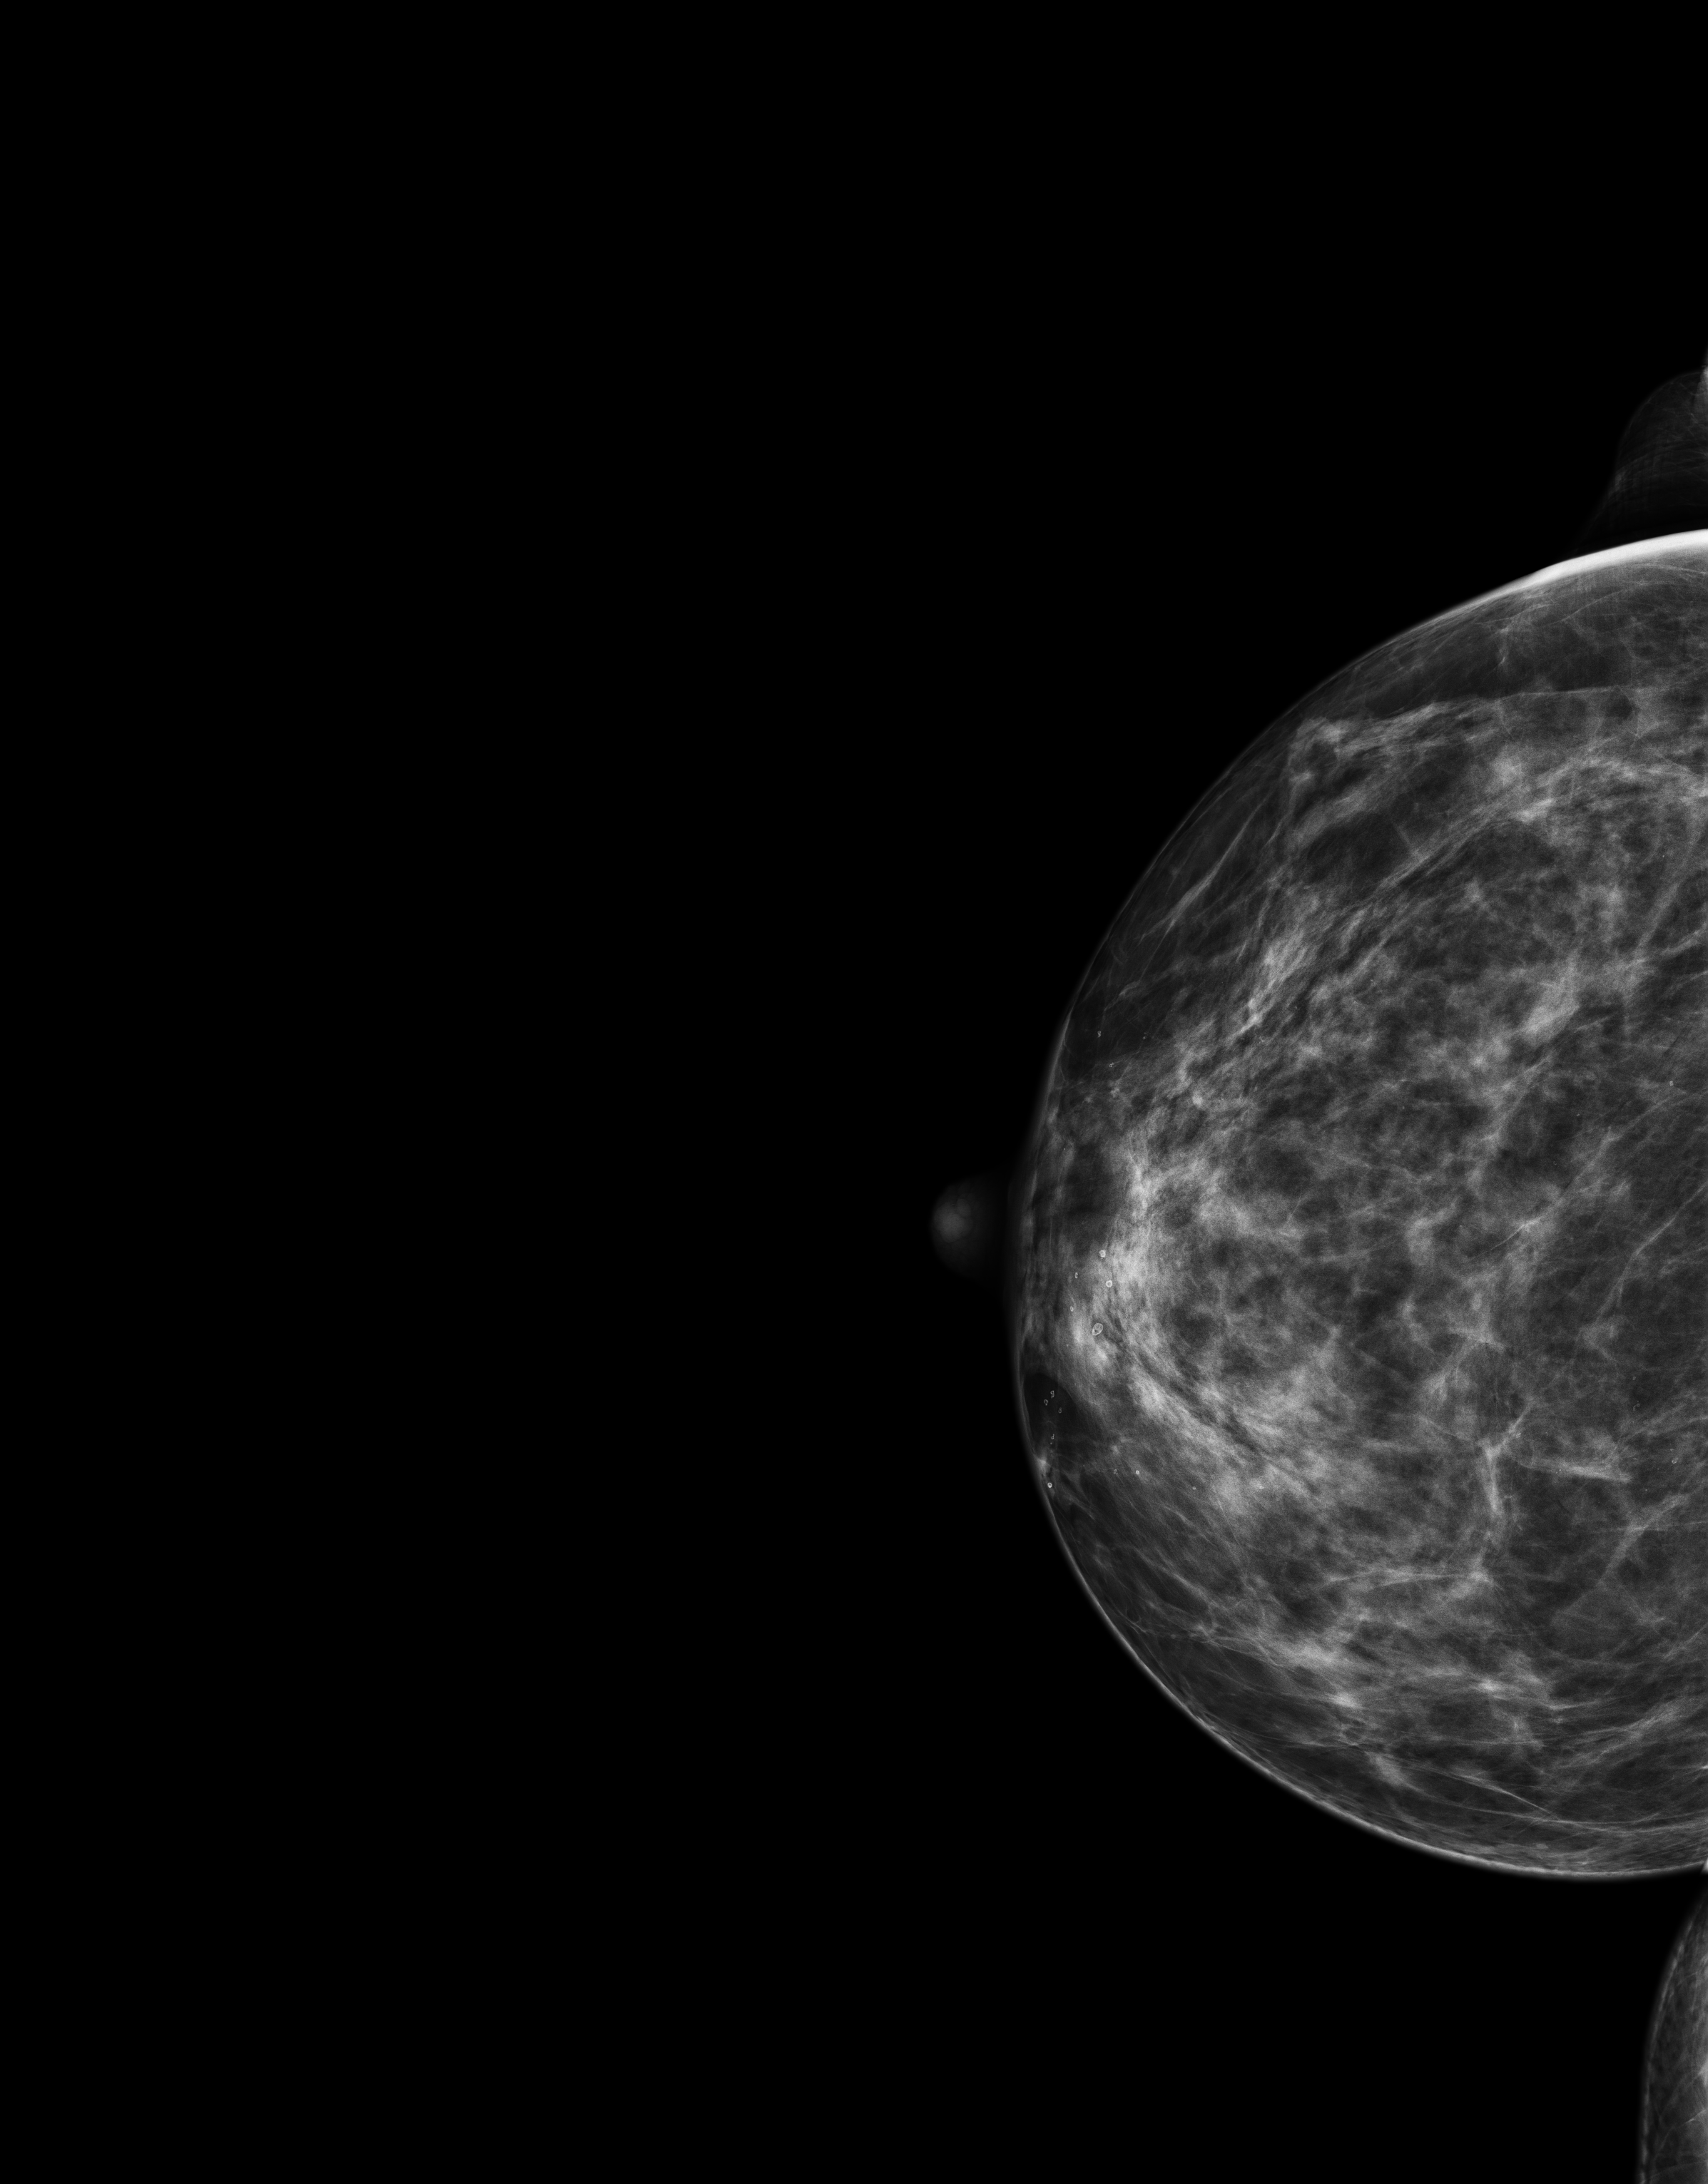
Digital mammogram (FFDM), right breast, craniocaudal (CC) view, annual screening mammography examination. Patient aged 46 years (female).
BI-RADS breast density category at the screening exam (both breasts, scale 1–4): 3. Final BI-RADS category for the screening round (tomosynthesis exam, both breasts): category 2. Recall: no recall after this screen.